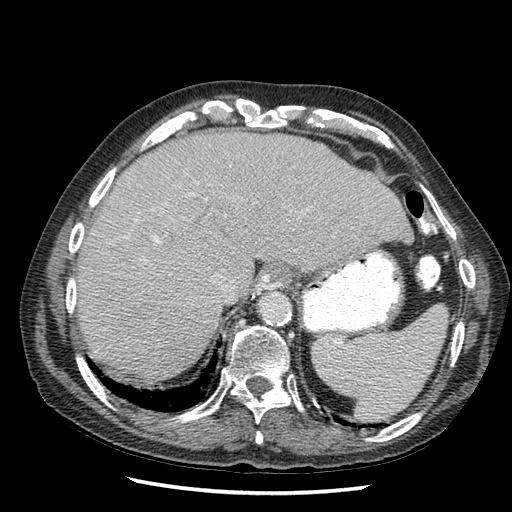
Contrast-enhanced abdominal CT (liver protocol), one axial slice. Position 43 of 67 along the scan axis. Reconstruction kernel STANDARD. Soft-tissue window (W 400 / L 40 HU). 2.5 mm slice thickness. 512 × 512 image matrix, field of view 360 × 360 mm. From the clinical record (not read from this slice): diagnosis: hepatocellular carcinoma (patient treated with transarterial chemoembolisation; whether this scan precedes or follows treatment is not stated here); TNM stage (as recorded): Stage-I; Child-Pugh class: A; tumour differentiation: moderately differentiated; tumour nodularity: uninodular.
Outlined on this slice (semi-automatically segmented with operator editing):
- liver parenchyma outside the tumour (the mass and vessels are separate outlines, so this box may not span the whole liver): bounding box [x1, y1, x2, y2] px = [77, 130, 412, 382]
- liver vessels: [123, 183, 197, 245]